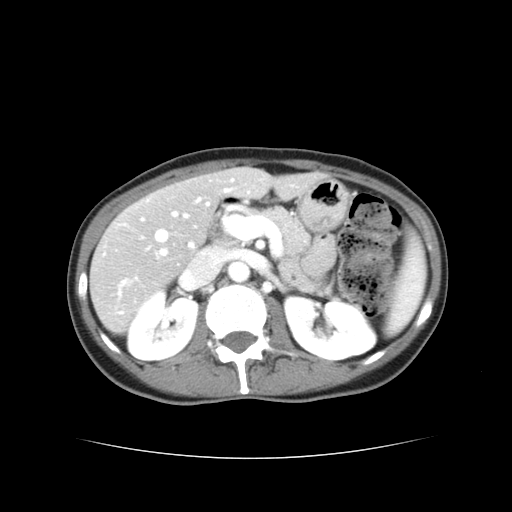
Contrast-enhanced abdominal CT, one axial slice; position 19 of 38 along the scan axis; reconstruction kernel STANDARD; 120 kVp; intravenous contrast given; soft-tissue window (W 400 / L 40 HU); 5 mm slice thickness; 512 × 512 image matrix, field of view 340 × 340 mm. Female patient, age 54 years. Case-level facts recorded for this patient, not image findings: diagnosis: colorectal cancer liver metastases, imaged before liver resection; multiple liver metastases: yes; largest metastasis: 1.1 cm; disease in both lobes: yes.
Annotated regions visible in this slice (manually delineated by an expert):
- hepatic veins: bounding box <157,190,229,241> (left, top, right, bottom; pixels)
- liver: <91,170,315,330>
- planned liver remnant (the part of the liver to remain after resection): <219,170,312,199>
- portal vein (with intrahepatic branches): <161,180,233,256>